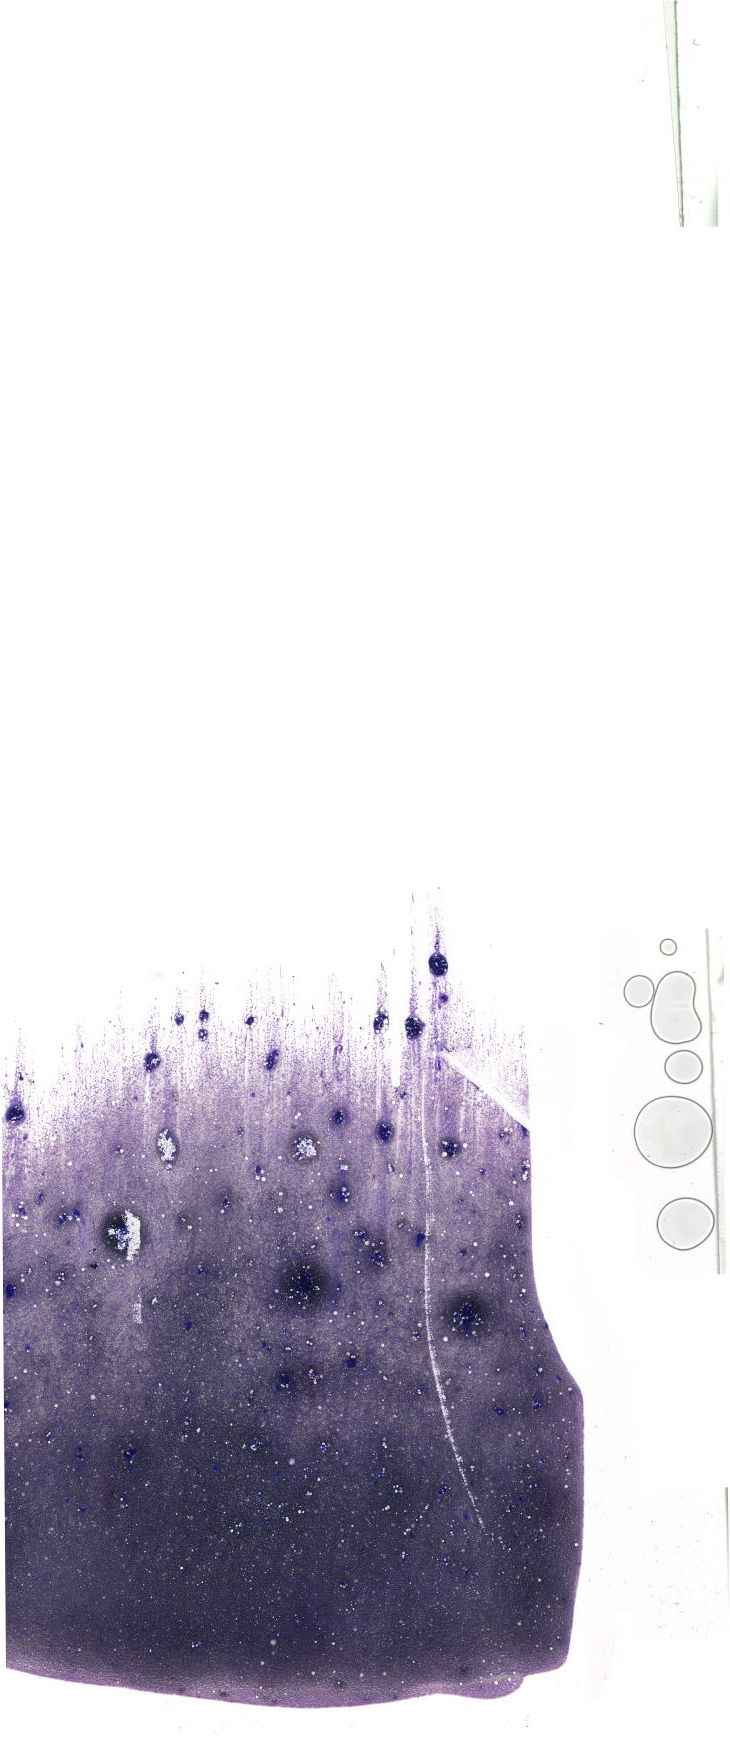
Whole-slide image of a May-Grünwald–Giemsa-stained bone marrow aspirate smear, shown as a low-resolution overview of the whole scanned area (about 20.7 x 49.3 mm). Patient sex: male.
Diagnosis: Chronic Phase Chronic Myeloid Leukemia, BCR-ABL1 Positive.